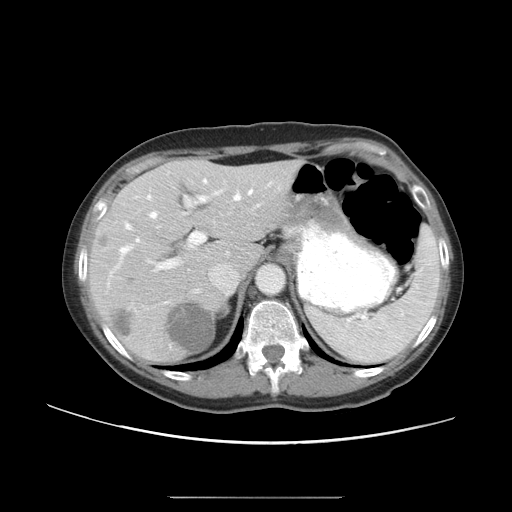
Contrast-enhanced abdominal CT, one axial slice; slice 33 of 50 in the series (ordered by position); reconstruction kernel STANDARD; 120 kVp; intravenous contrast given; soft-tissue window (W 400 / L 40 HU); 5 mm slice thickness; 512 × 512 image matrix, field of view 389 × 389 mm. Female patient, age 58 years. Case-level facts recorded for this patient, not image findings: diagnosis: colorectal cancer liver metastases, imaged before liver resection; multiple liver metastases: yes; largest metastasis: 7.3 cm; disease in both lobes: yes.
Structures marked on this image (outlined manually by an expert reader):
- hepatic veins: box from (x=121, y=178) to (x=254, y=253) px
- liver: (x=91, y=162)–(x=291, y=361)
- planned liver remnant (the part of the liver to remain after resection): (x=171, y=162)–(x=291, y=268)
- portal vein (with intrahepatic branches): (x=146, y=181)–(x=276, y=269)
- liver metastasis: (x=169, y=303)–(x=212, y=354)
- liver metastasis: (x=113, y=313)–(x=132, y=337)
- liver metastasis: (x=99, y=240)–(x=107, y=247)
- liver metastasis: (x=99, y=239)–(x=108, y=247)
- liver metastasis: (x=99, y=236)–(x=106, y=247)